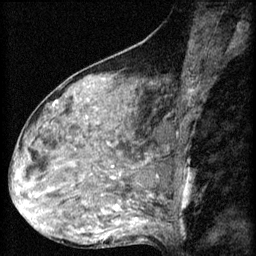
Breast MRI (dynamic contrast-enhanced), one sagittal slice. Slice 30 of 60 in the series (ordered by position). 3 images stored at this slice position (order not interpretable as contrast timing). 1.5 T. TE 4.2 ms, TR 8.2 ms. 256 × 256 image matrix, field of view 180 × 180 mm. Female patient, age 48 years.
Outlined on this slice (semi-automatically segmented with operator editing):
- analysis volume of interest (the breast-tissue region the enhancement analysis was run in; not a lesion): bounding box <48,160,125,217> (left, top, right, bottom; pixels)
- tumour enhancement mask (voxels above the 70 % enhancement threshold inside the analysis volume of interest): <112,166,117,207>